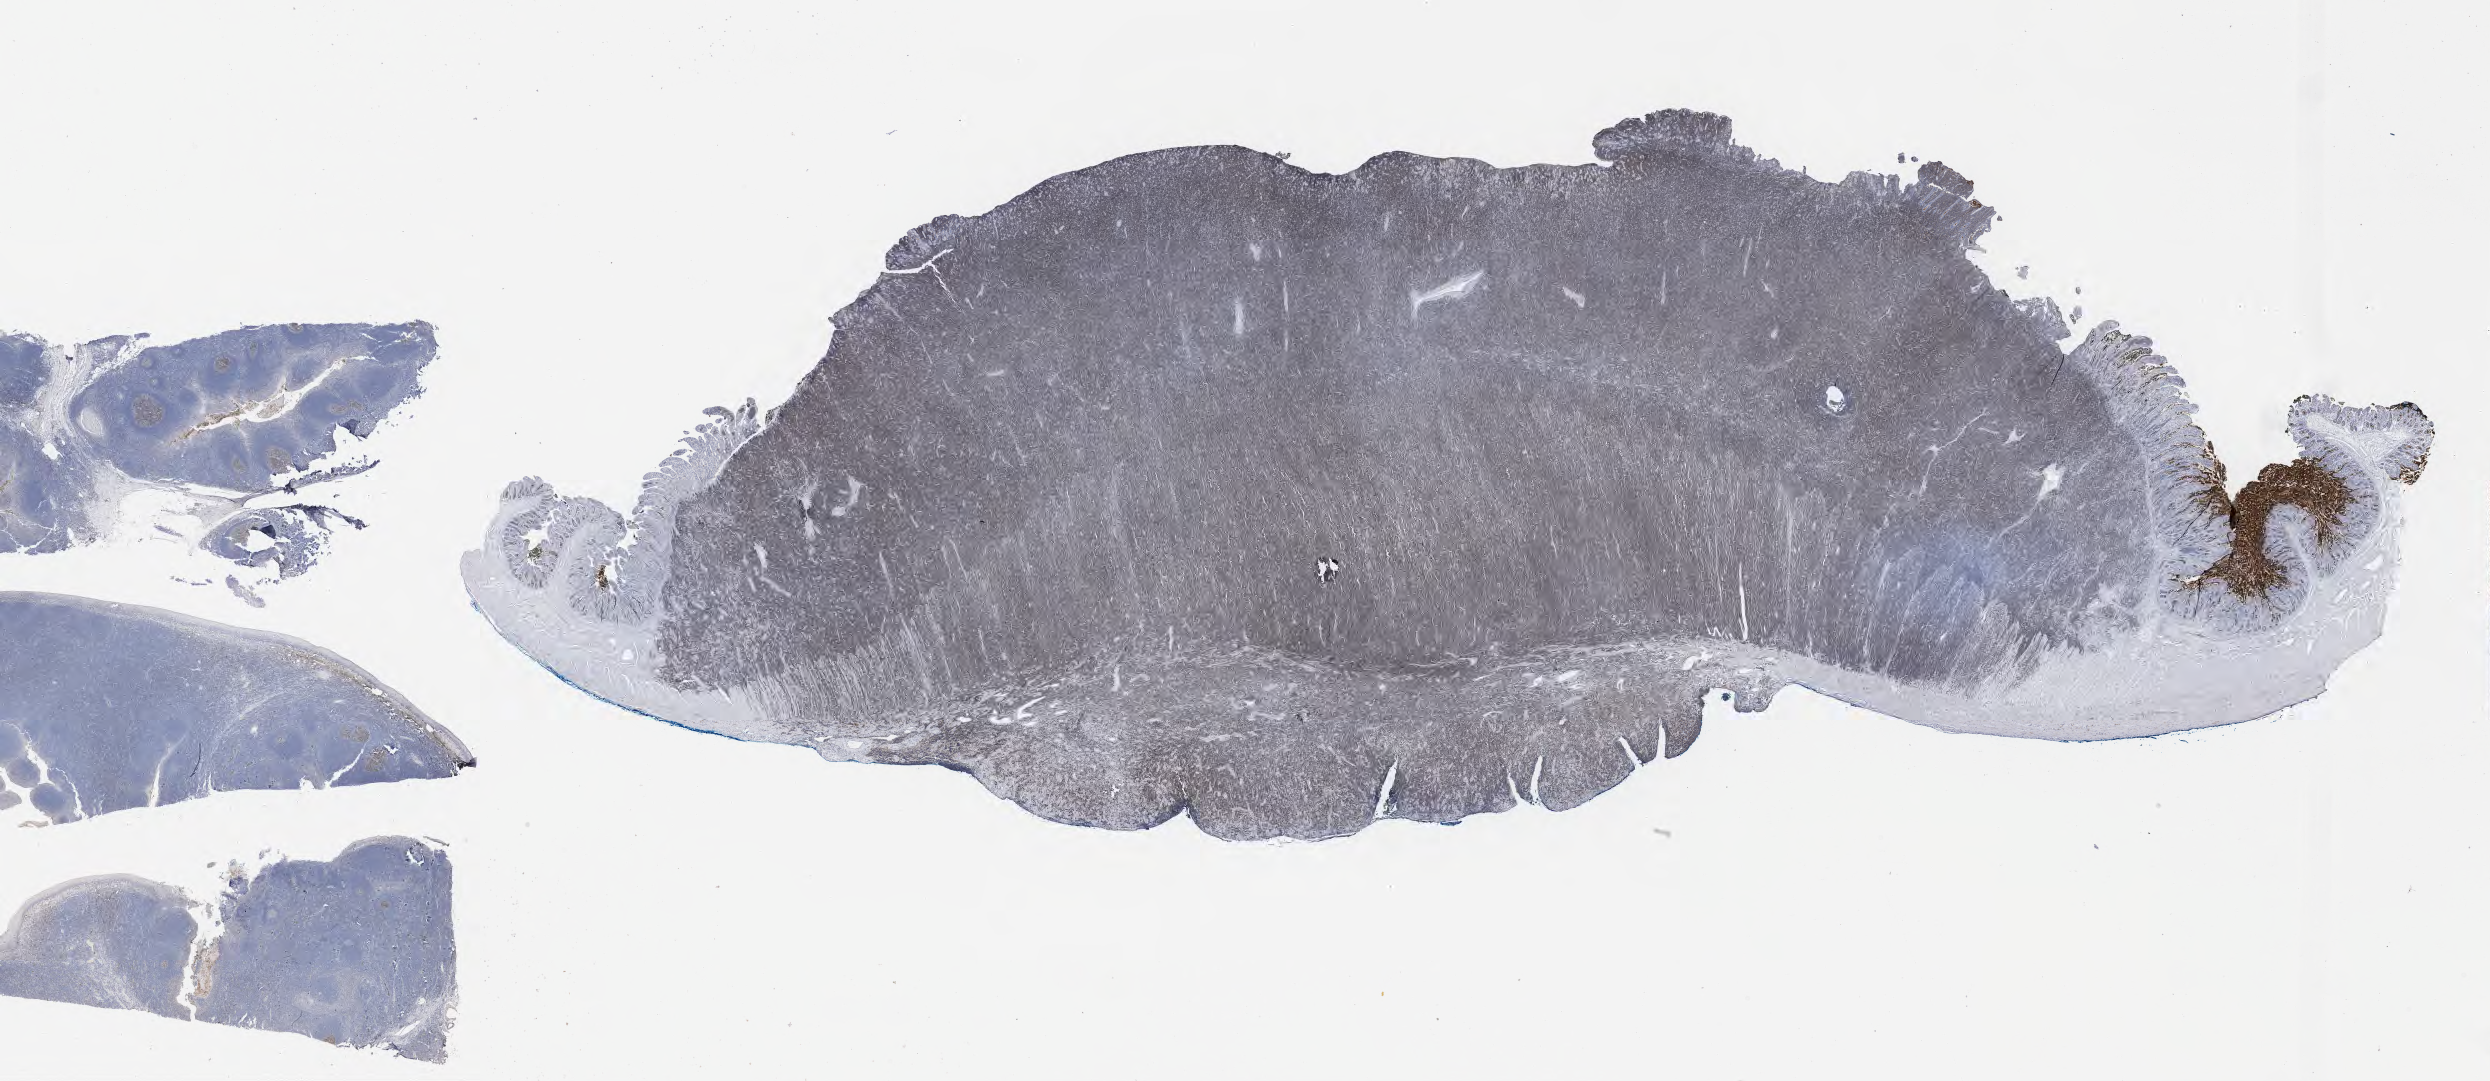
Whole-slide image, immunohistochemical stain for CD10 — low-resolution overview of the scanned area, about 40.2 x 17.5 mm; specimen: tumor tissue; site: small intestine. Patient: male, age at initial diagnosis 6 years.
* histologic diagnosis: Burkitt lymphoma, NOS